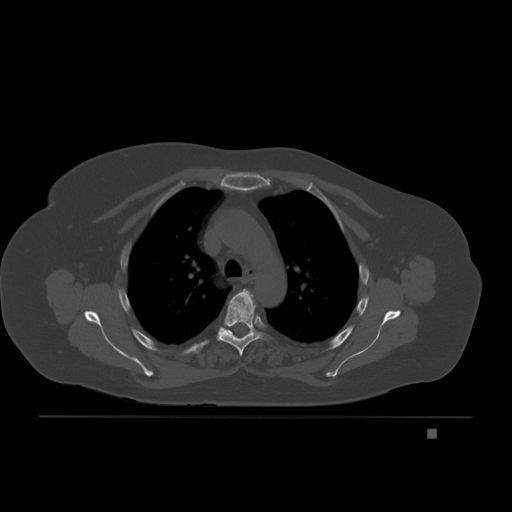
CT including the spine, one axial slice; position 152 of 221 along the scan axis; bone window (W 1800 / L 400 HU); 512 × 512 image matrix, field of view 474 × 474 mm. Female patient, age 63 years. Case-level facts recorded for this patient, not image findings: primary cancer: breast.
Annotated regions visible in this slice (semi-automatically segmented with operator editing):
- T4 vertebra: bounding box [x1, y1, x2, y2] px = [217, 289, 269, 356]